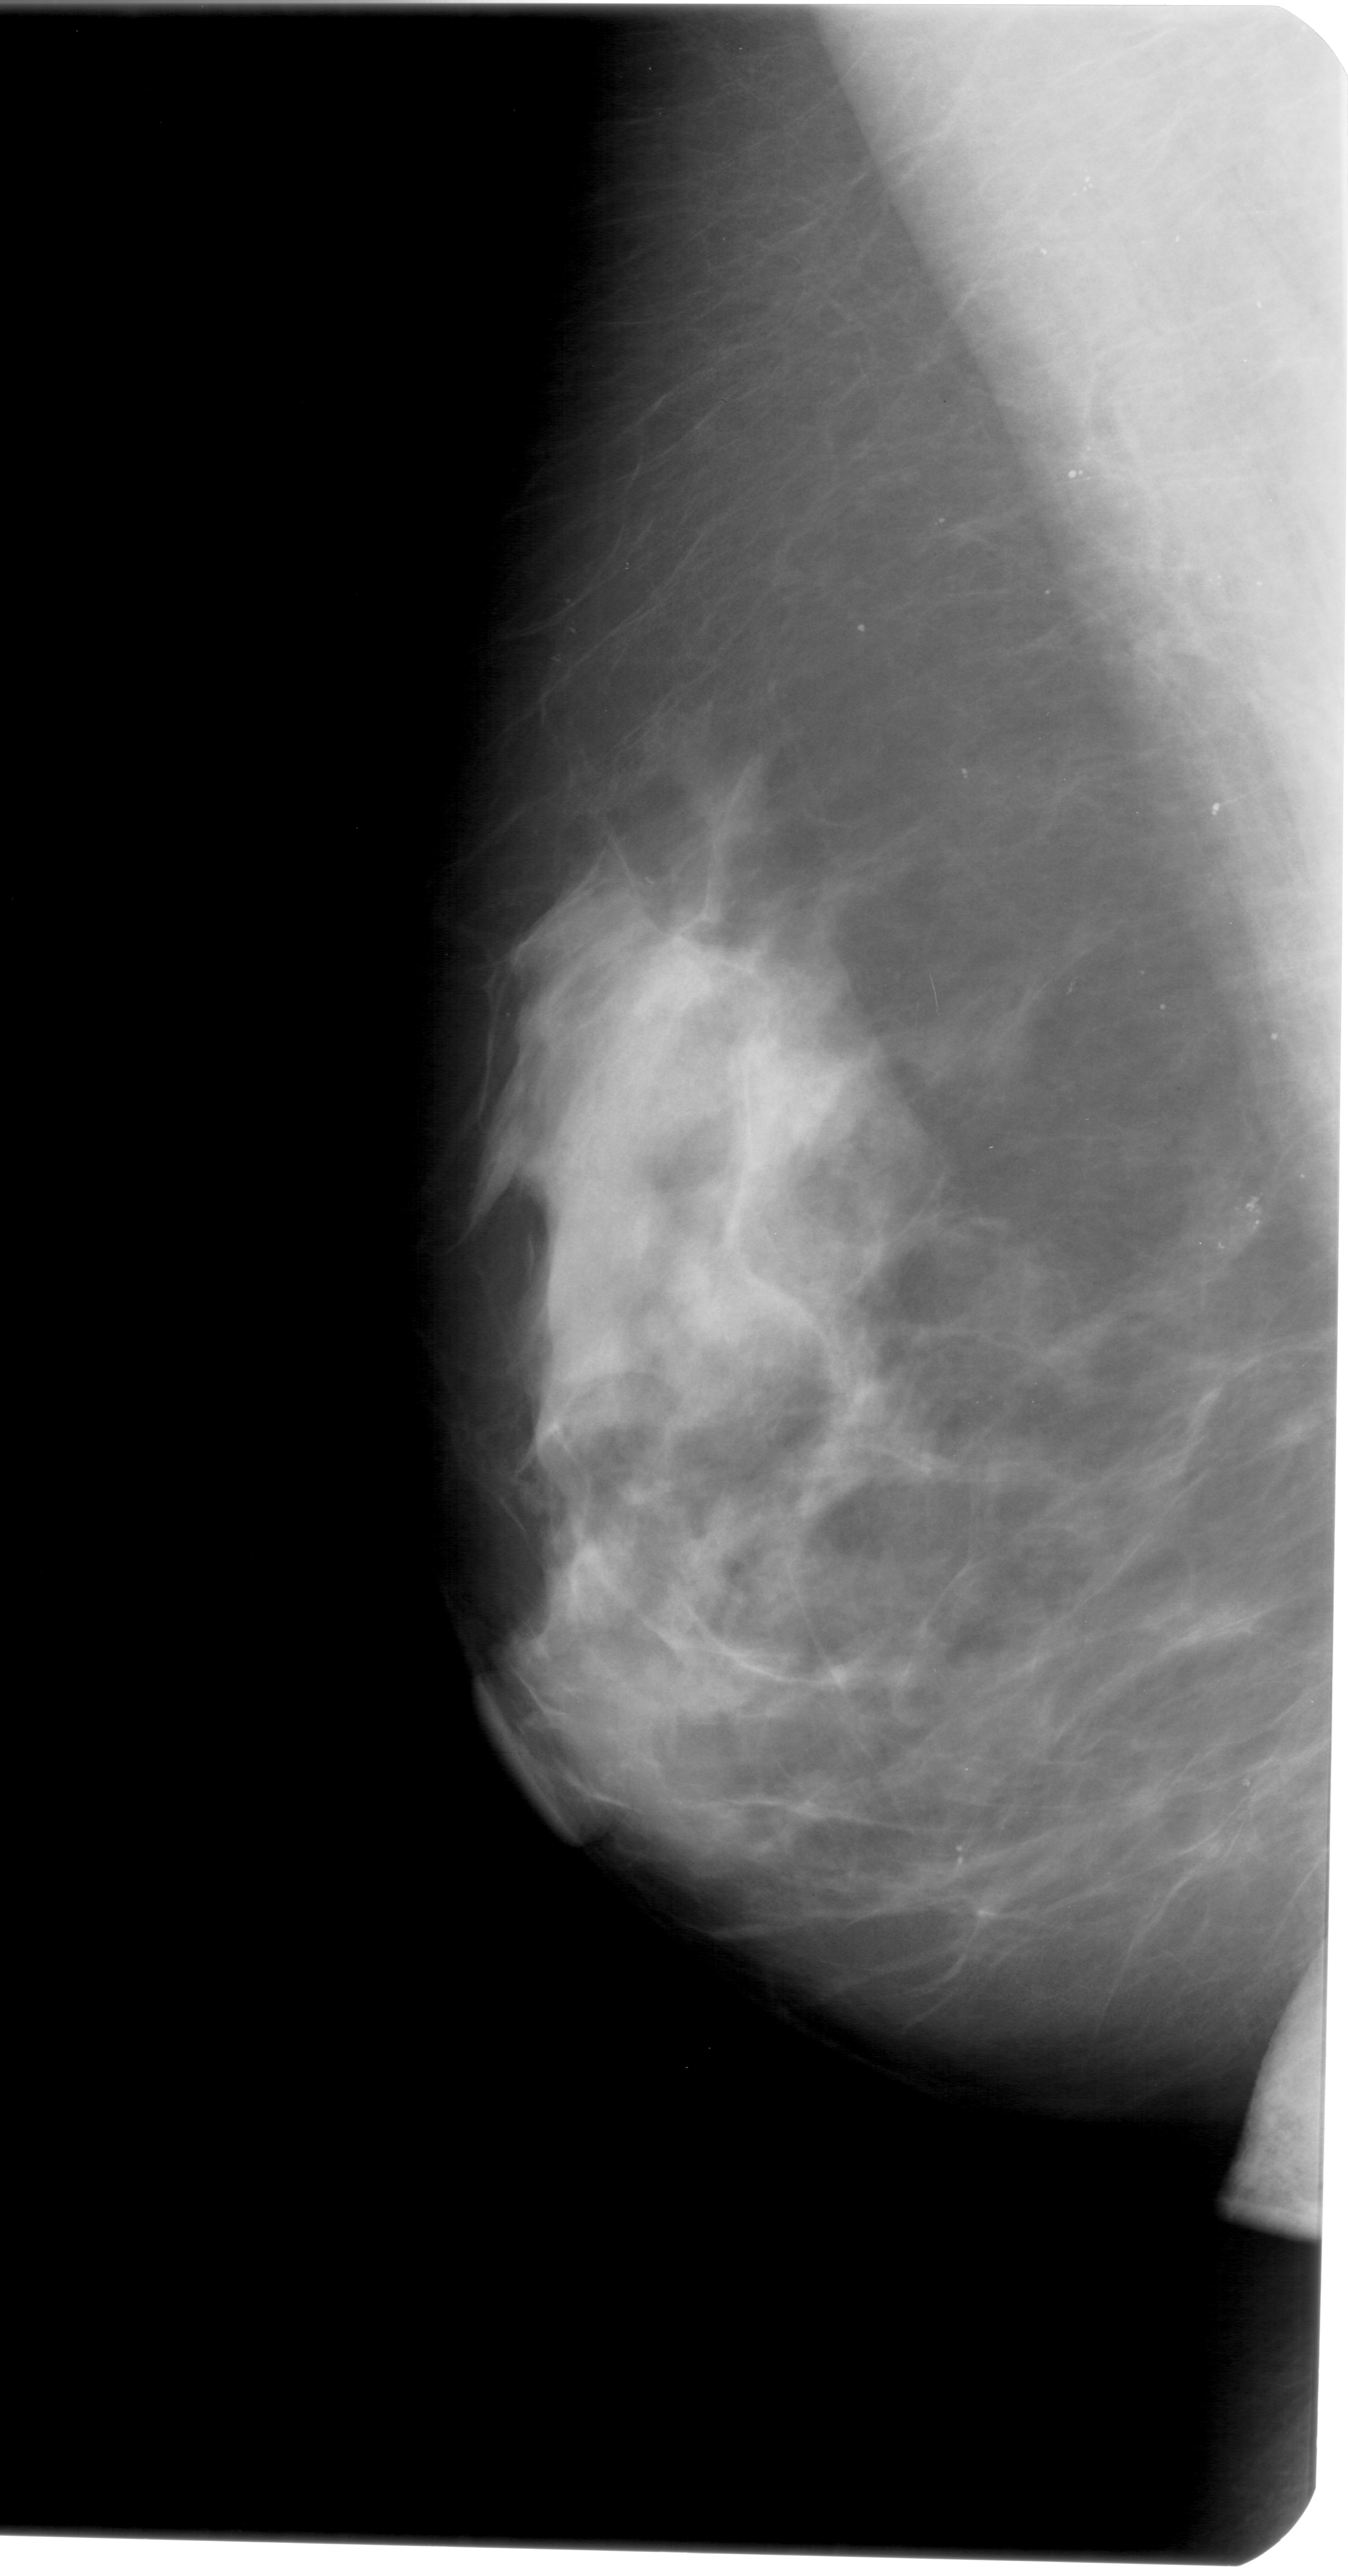
Scanned film-screen mammogram; left breast; mediolateral oblique (MLO) view; 1348 × 2576 image matrix.
Marked abnormalities (boxes around the expert regions of interest):
- calcifications, morphology pleomorphic, distribution clustered; BI-RADS assessment category 4; pathology result (as recorded, not read from the image): benign: box from (x=1178, y=1169) to (x=1275, y=1261) px